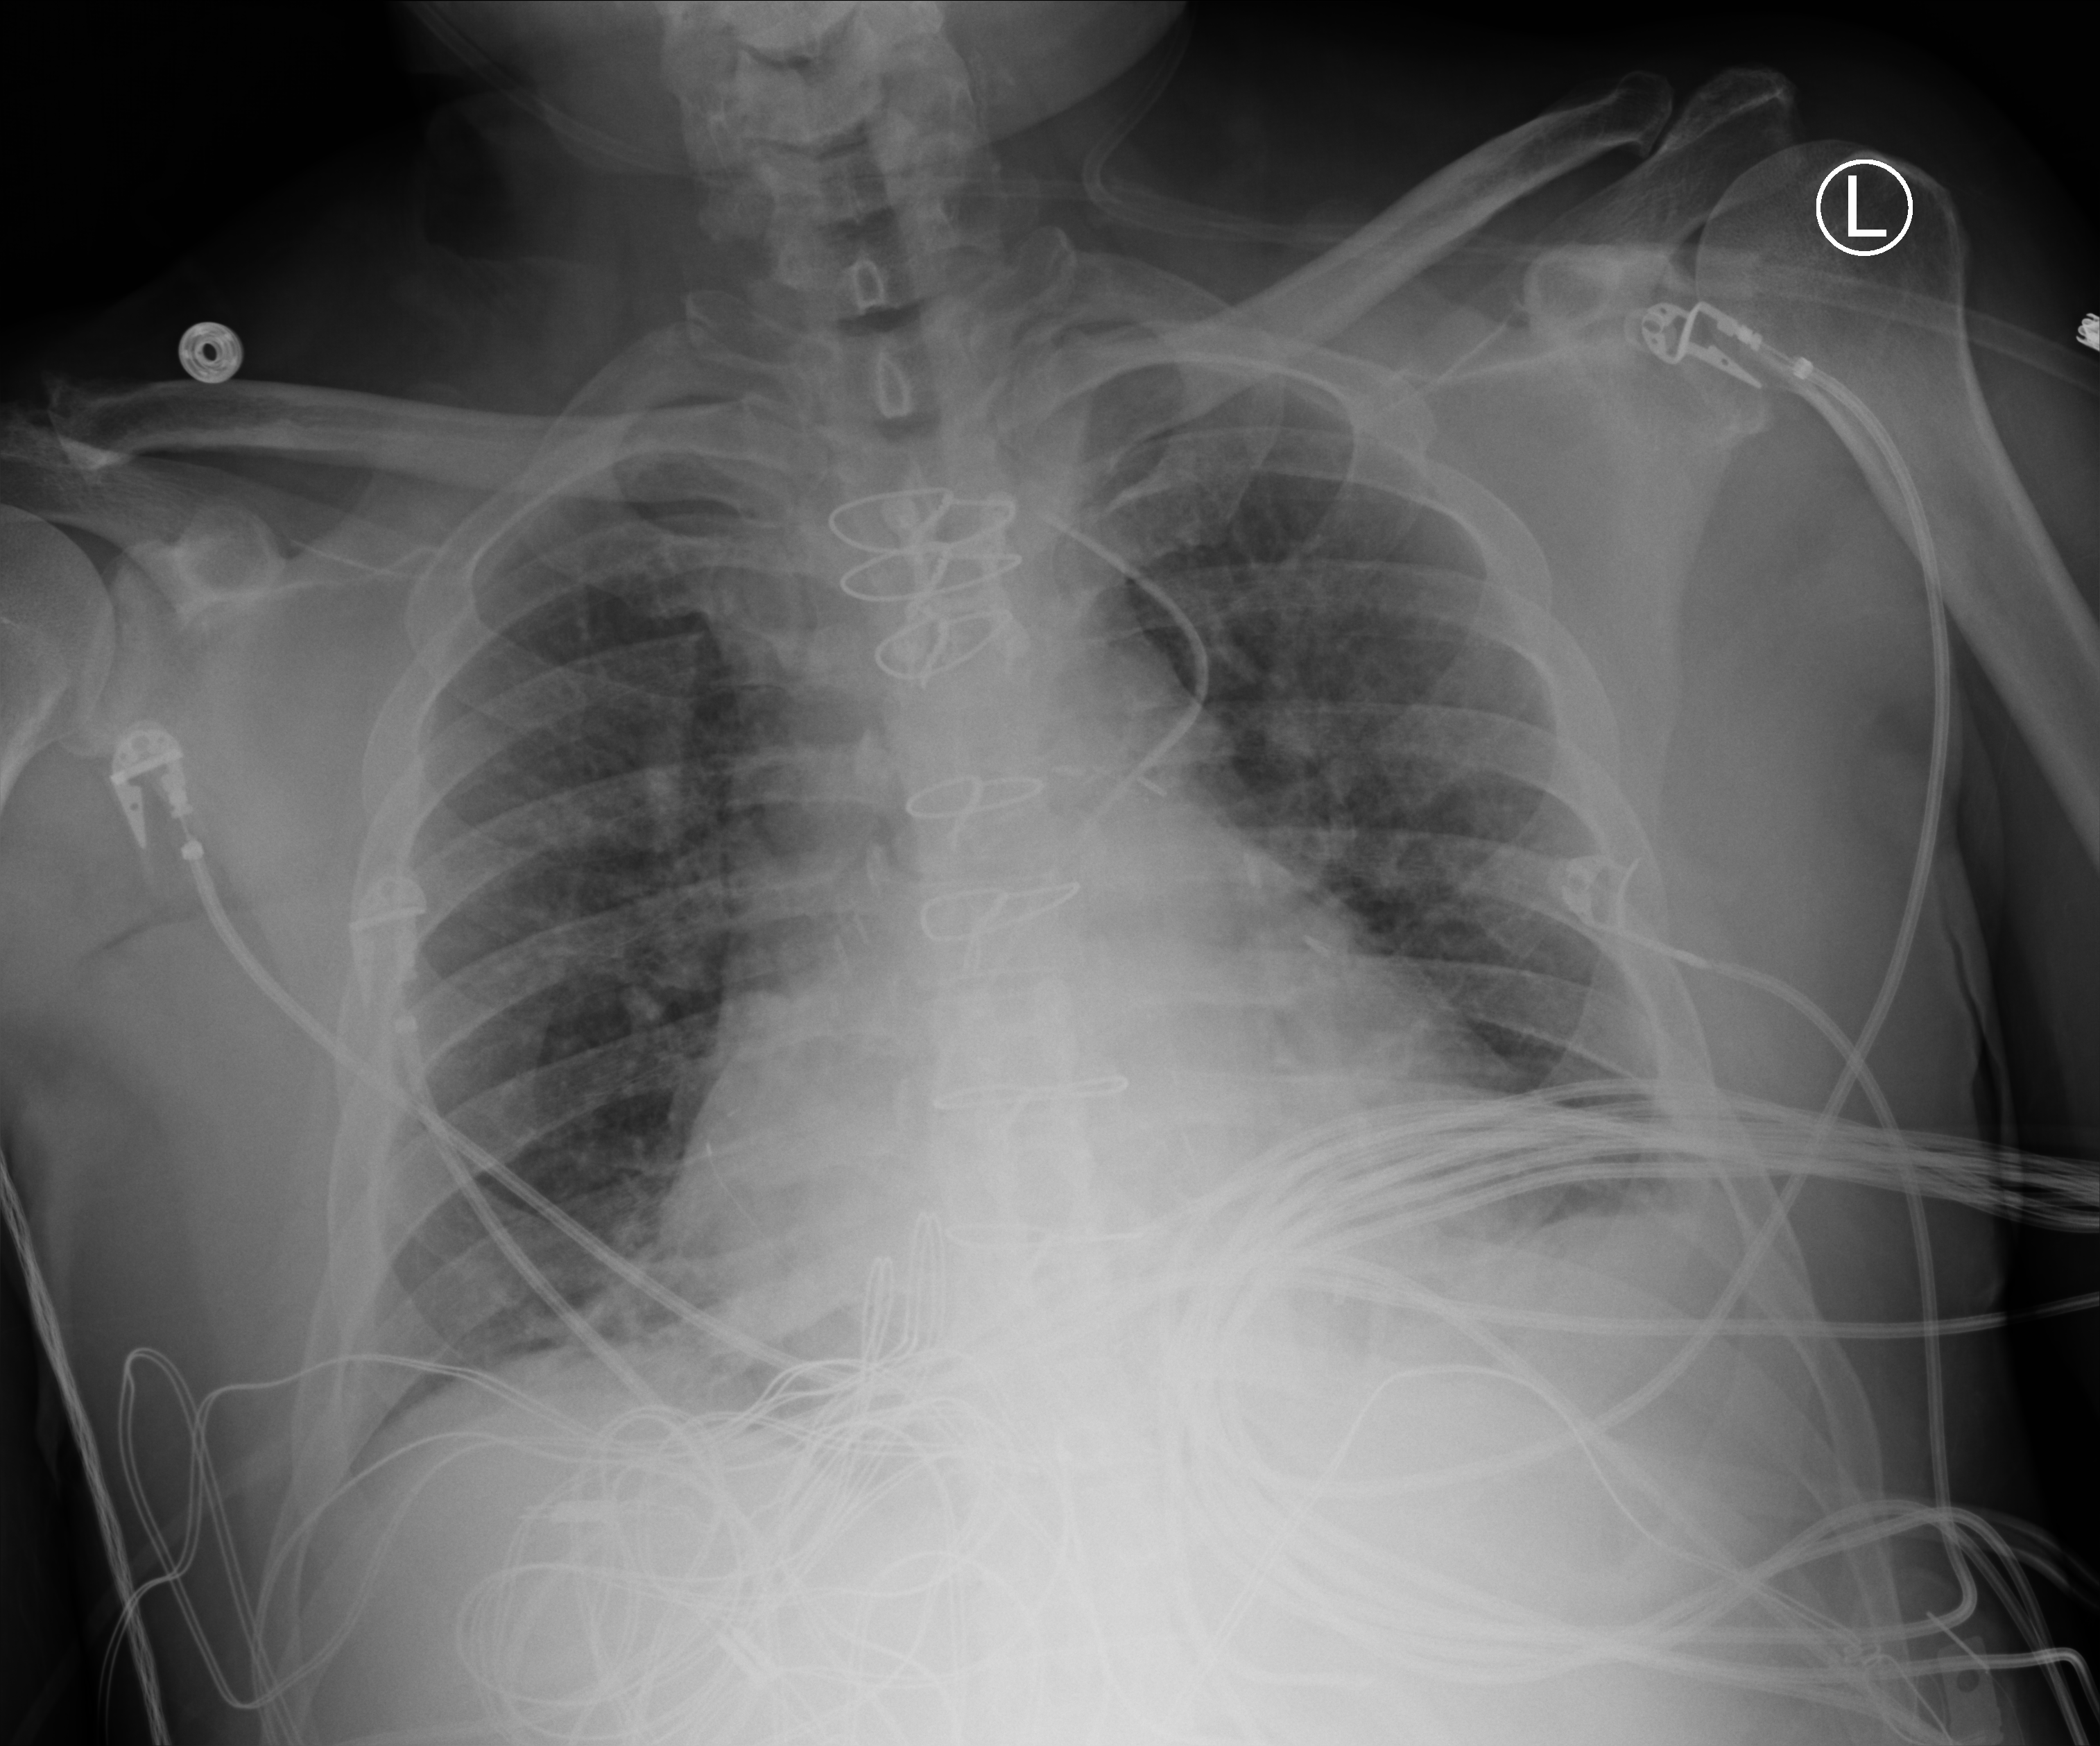
Chest X-ray (portable), anteroposterior (AP) projection. Male patient hospitalised with COVID-19, age 60–74 years.
Admission-level facts for this patient (not findings on this image; timing relative to this image not recorded): chronic kidney disease (admission record): no.